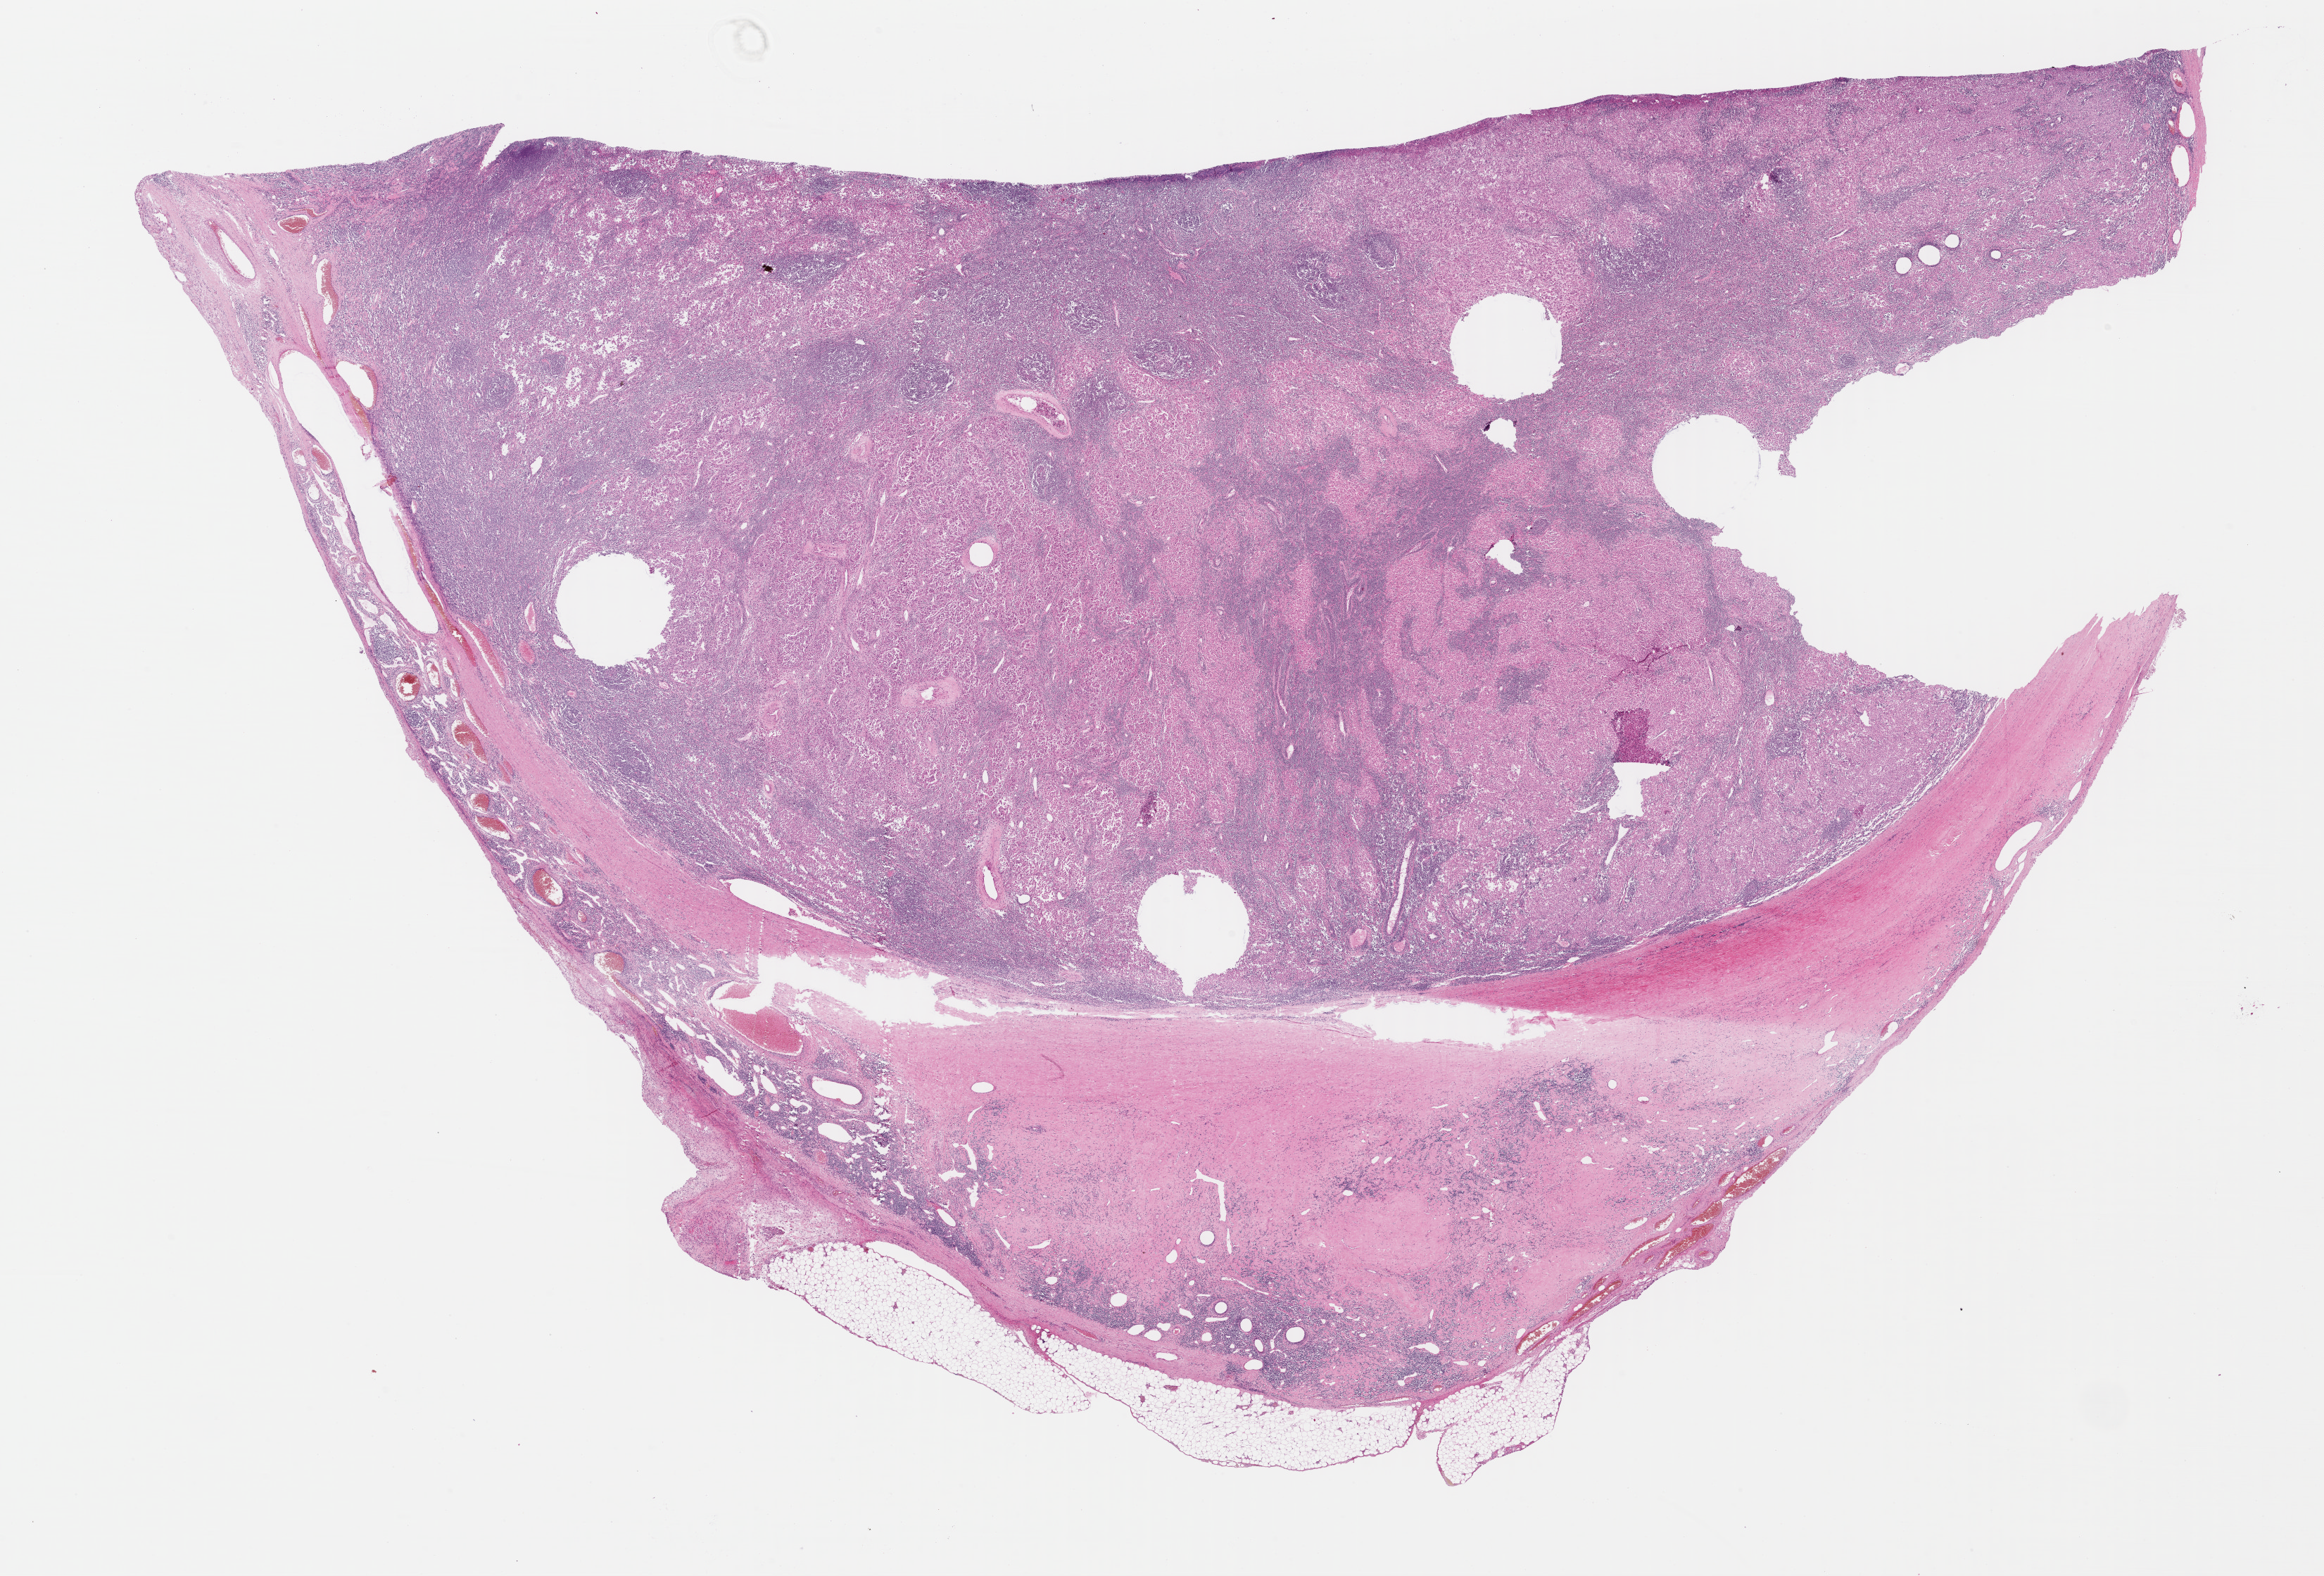
Digitized H&E tissue section (whole slide), low-resolution overview of the scanned area, about 26.0 x 17.6 mm (from a 40x scan), formalin-fixed paraffin-embedded (FFPE) diagnostic section, primary tumour sample from the skin. Patient: male, age at initial diagnosis 35 years.
Histologic diagnosis: Malignant melanoma, NOS.